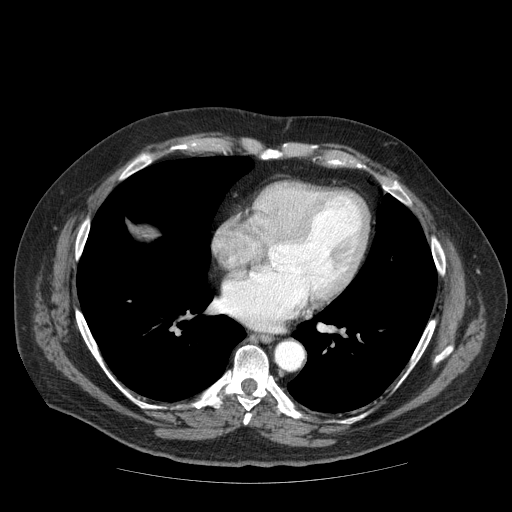
Contrast-enhanced abdominal CT (liver protocol), one axial slice. Position 76 of 85 along the scan axis. 120 kVp. Soft-tissue window (W 400 / L 40 HU). 2.5 mm slice thickness. 512 × 512 image matrix, field of view 420 × 420 mm. From the clinical record (not read from this slice): diagnosis: hepatocellular carcinoma (patient treated with transarterial chemoembolisation; whether this scan precedes or follows treatment is not stated here); TNM stage (as recorded): Stage-IIIA; Child-Pugh class: A; tumour nodularity: multinodular; tumour size: 7 cm.
Structures marked on this image (semi-automatically segmented with operator editing):
- liver parenchyma outside the tumour (the mass and vessels are separate outlines, so this box may not span the whole liver): box from (x=136, y=228) to (x=155, y=238) px